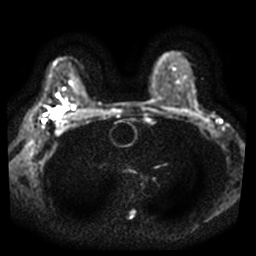
Breast MRI, one axial slice. Slice 24 of 37 in the series (ordered by position). Diffusion-weighted series; image 2 of 4 stored at this slice position (different b-values; order by instance number). 3 T. 5 mm slice thickness. 256 × 256 image matrix, field of view 340 × 340 mm. Female patient.
Outlined on this slice (outlined manually by an expert reader):
- tumour on diffusion-weighted imaging: bounding box <52,110,61,119> (left, top, right, bottom; pixels)